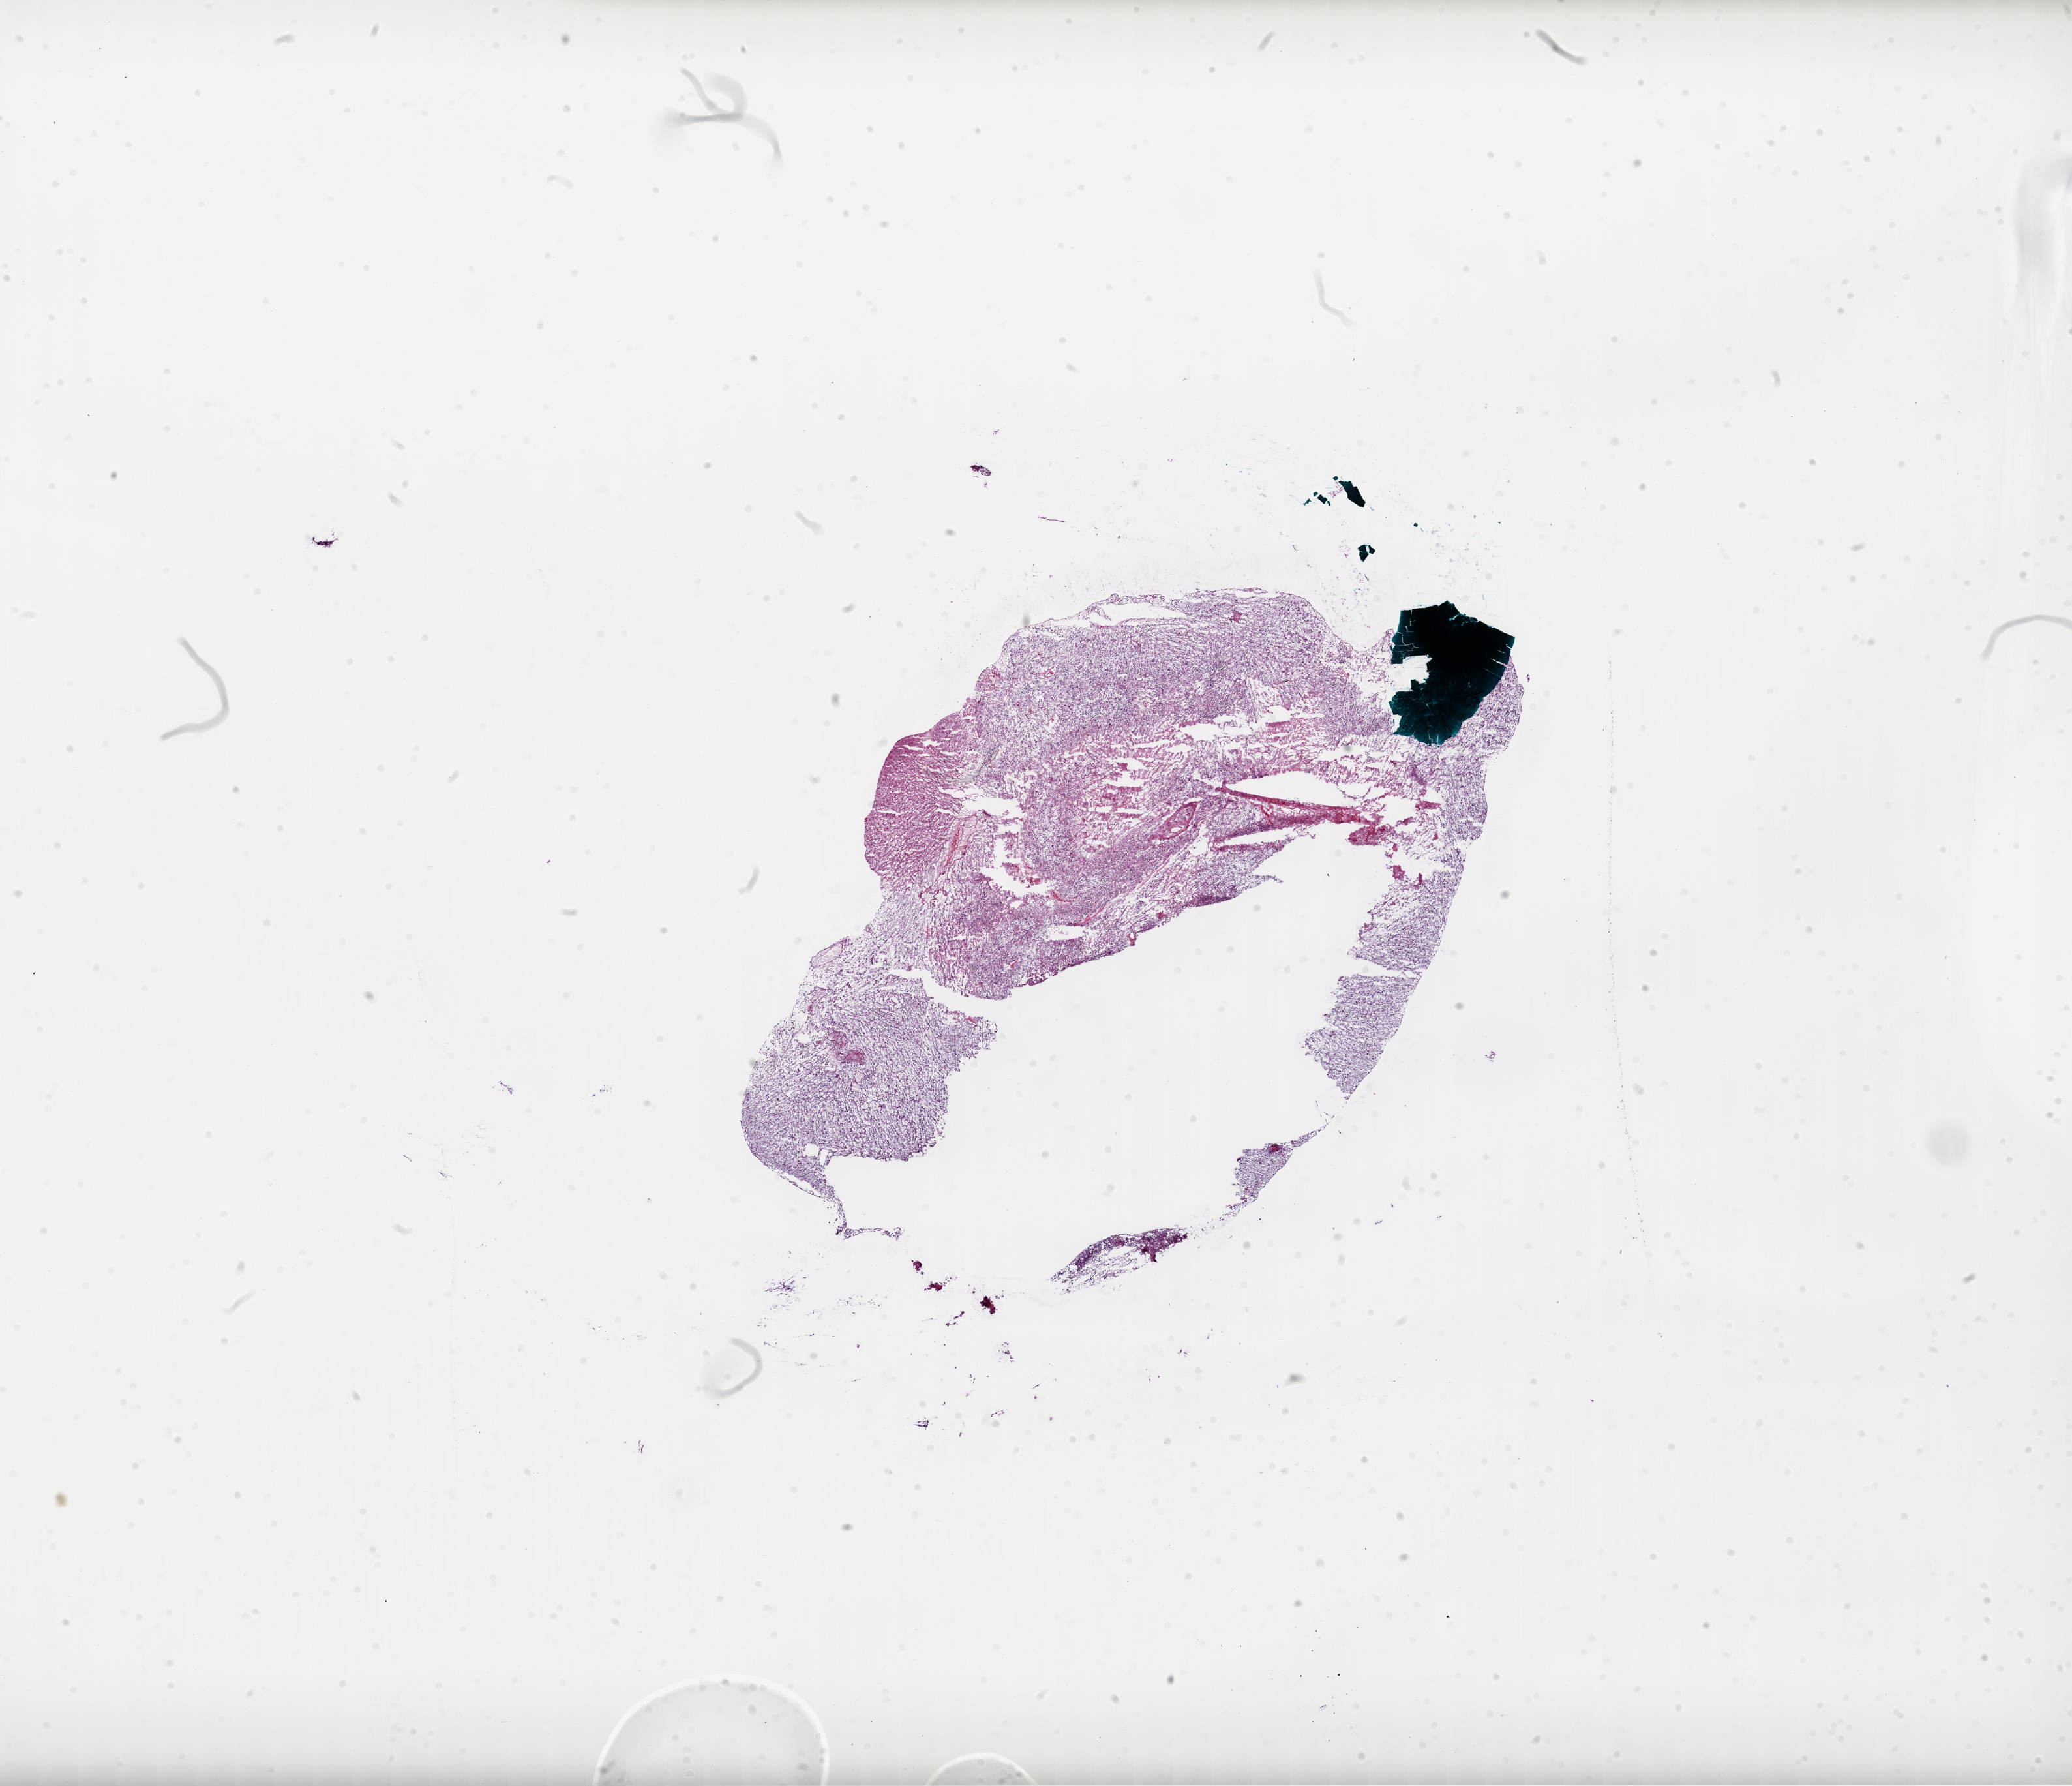
Whole-slide histology image, Hematoxylin and eosin (H&E) stained — shown as a low-resolution overview of the whole scanned area (about 25.6 x 22.1 mm). Frozen section from the bottom of the tissue portion. Primary tumour sample from the brain. Female patient; age at initial diagnosis 68 years.
Pathologic diagnosis: Glioblastoma.